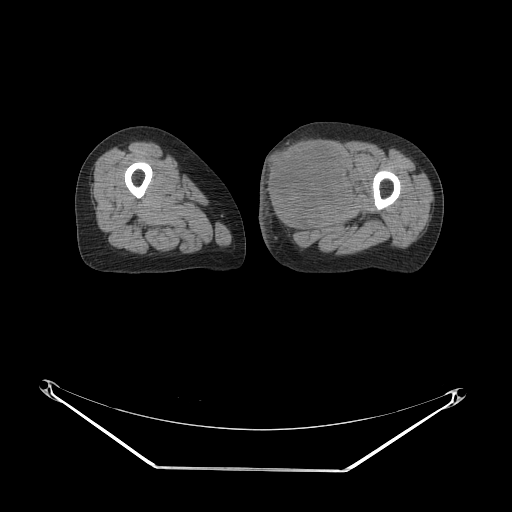
CT of an extremity soft-tissue mass (from a PET/CT study), one axial slice; slice 35 of 91 in the series (ordered by position); soft-tissue window (W 400 / L 40 HU); 3.75 mm slice thickness; 512 × 512 image matrix, field of view 500 × 500 mm. Female patient. Case-level facts recorded for this patient, not image findings: histological type: pleomorphic leiomyosarcoma; grade: high; site of the primary tumour: left thigh.
Annotated regions visible in this slice (expert contour drawn on MRI and transferred to this co-registered scan by the dataset authors):
- gross tumour volume including surrounding oedema: bounding box (x1, y1, x2, y2) in pixels: (263, 137, 357, 234)
- gross tumour volume (mass): (263, 137, 352, 234)